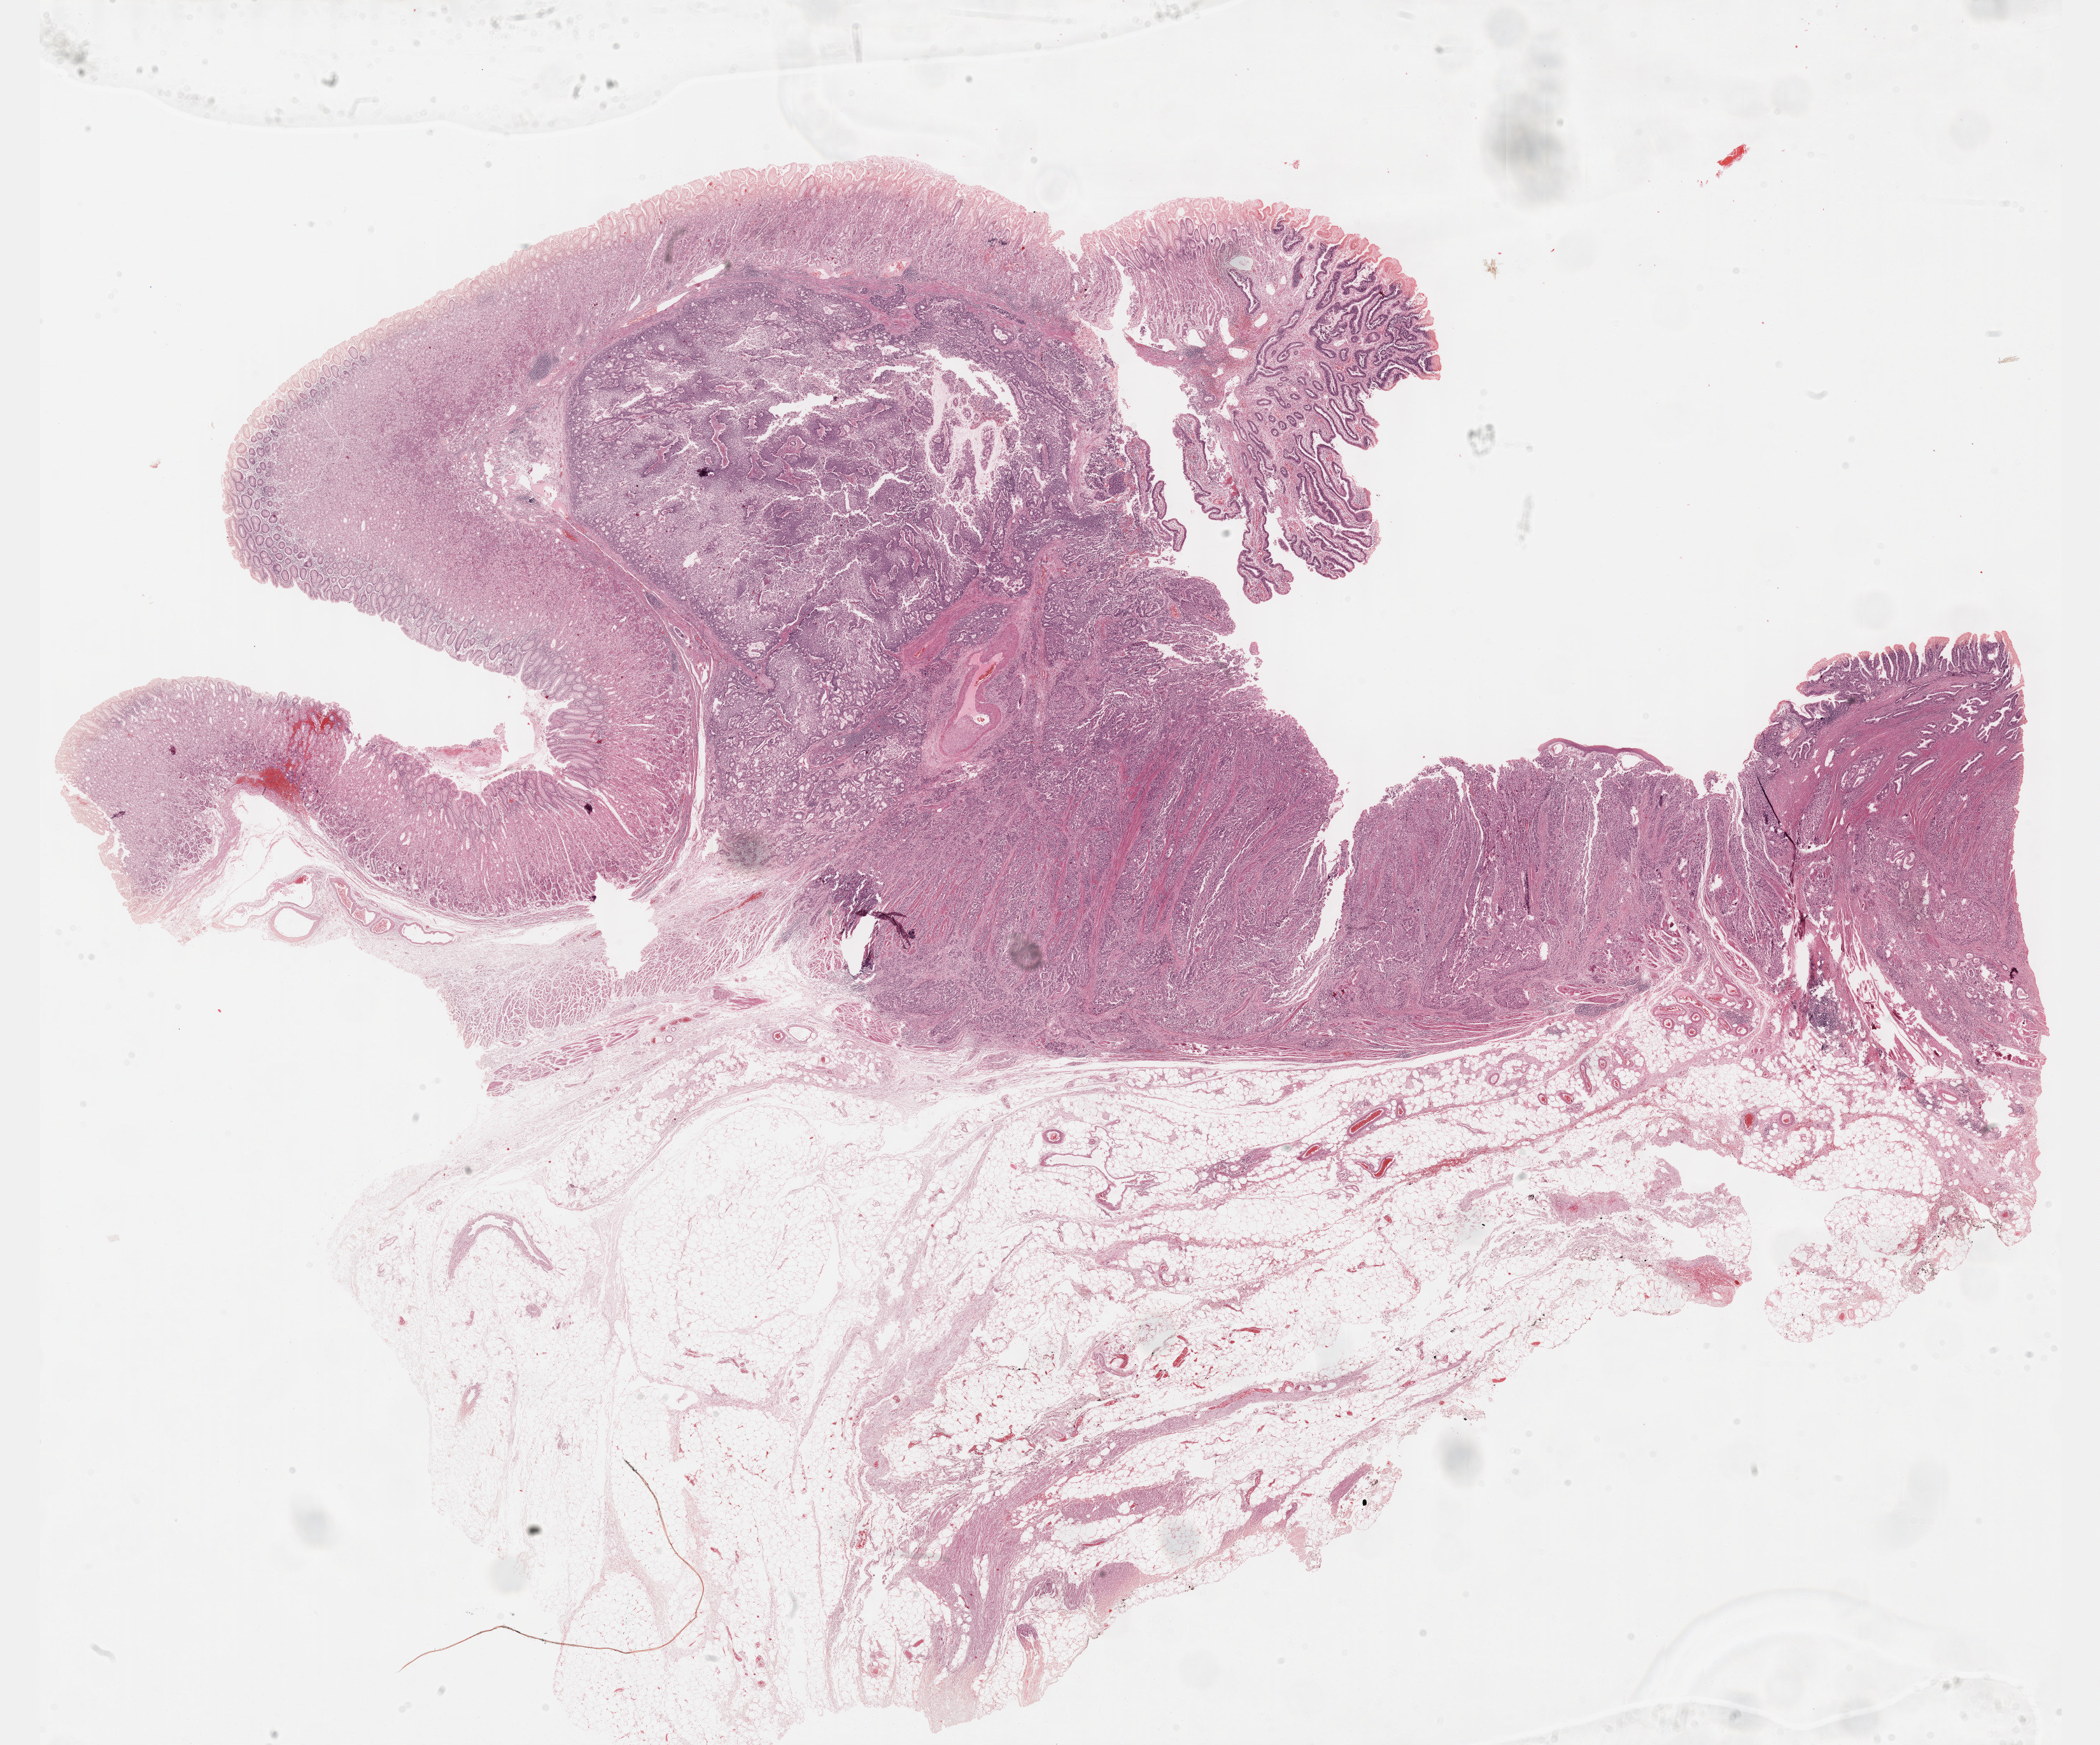
H&E whole-slide image — shown as a low-resolution overview of the whole scanned area (about 26.7 x 22.1 mm, acquisition: 40x scan), formalin-fixed paraffin-embedded (FFPE) diagnostic section, sample: primary tumour, esophagus. Male patient; age at initial diagnosis 66 years. Histologic grade: G2 (moderately differentiated).
- TNM: T3 N1 M0
- lymph nodes positive (case pathology): 4 of 19 examined
- AJCC pathologic stage: III
- diagnosis: Adenocarcinoma, NOS (lower third of esophagus)